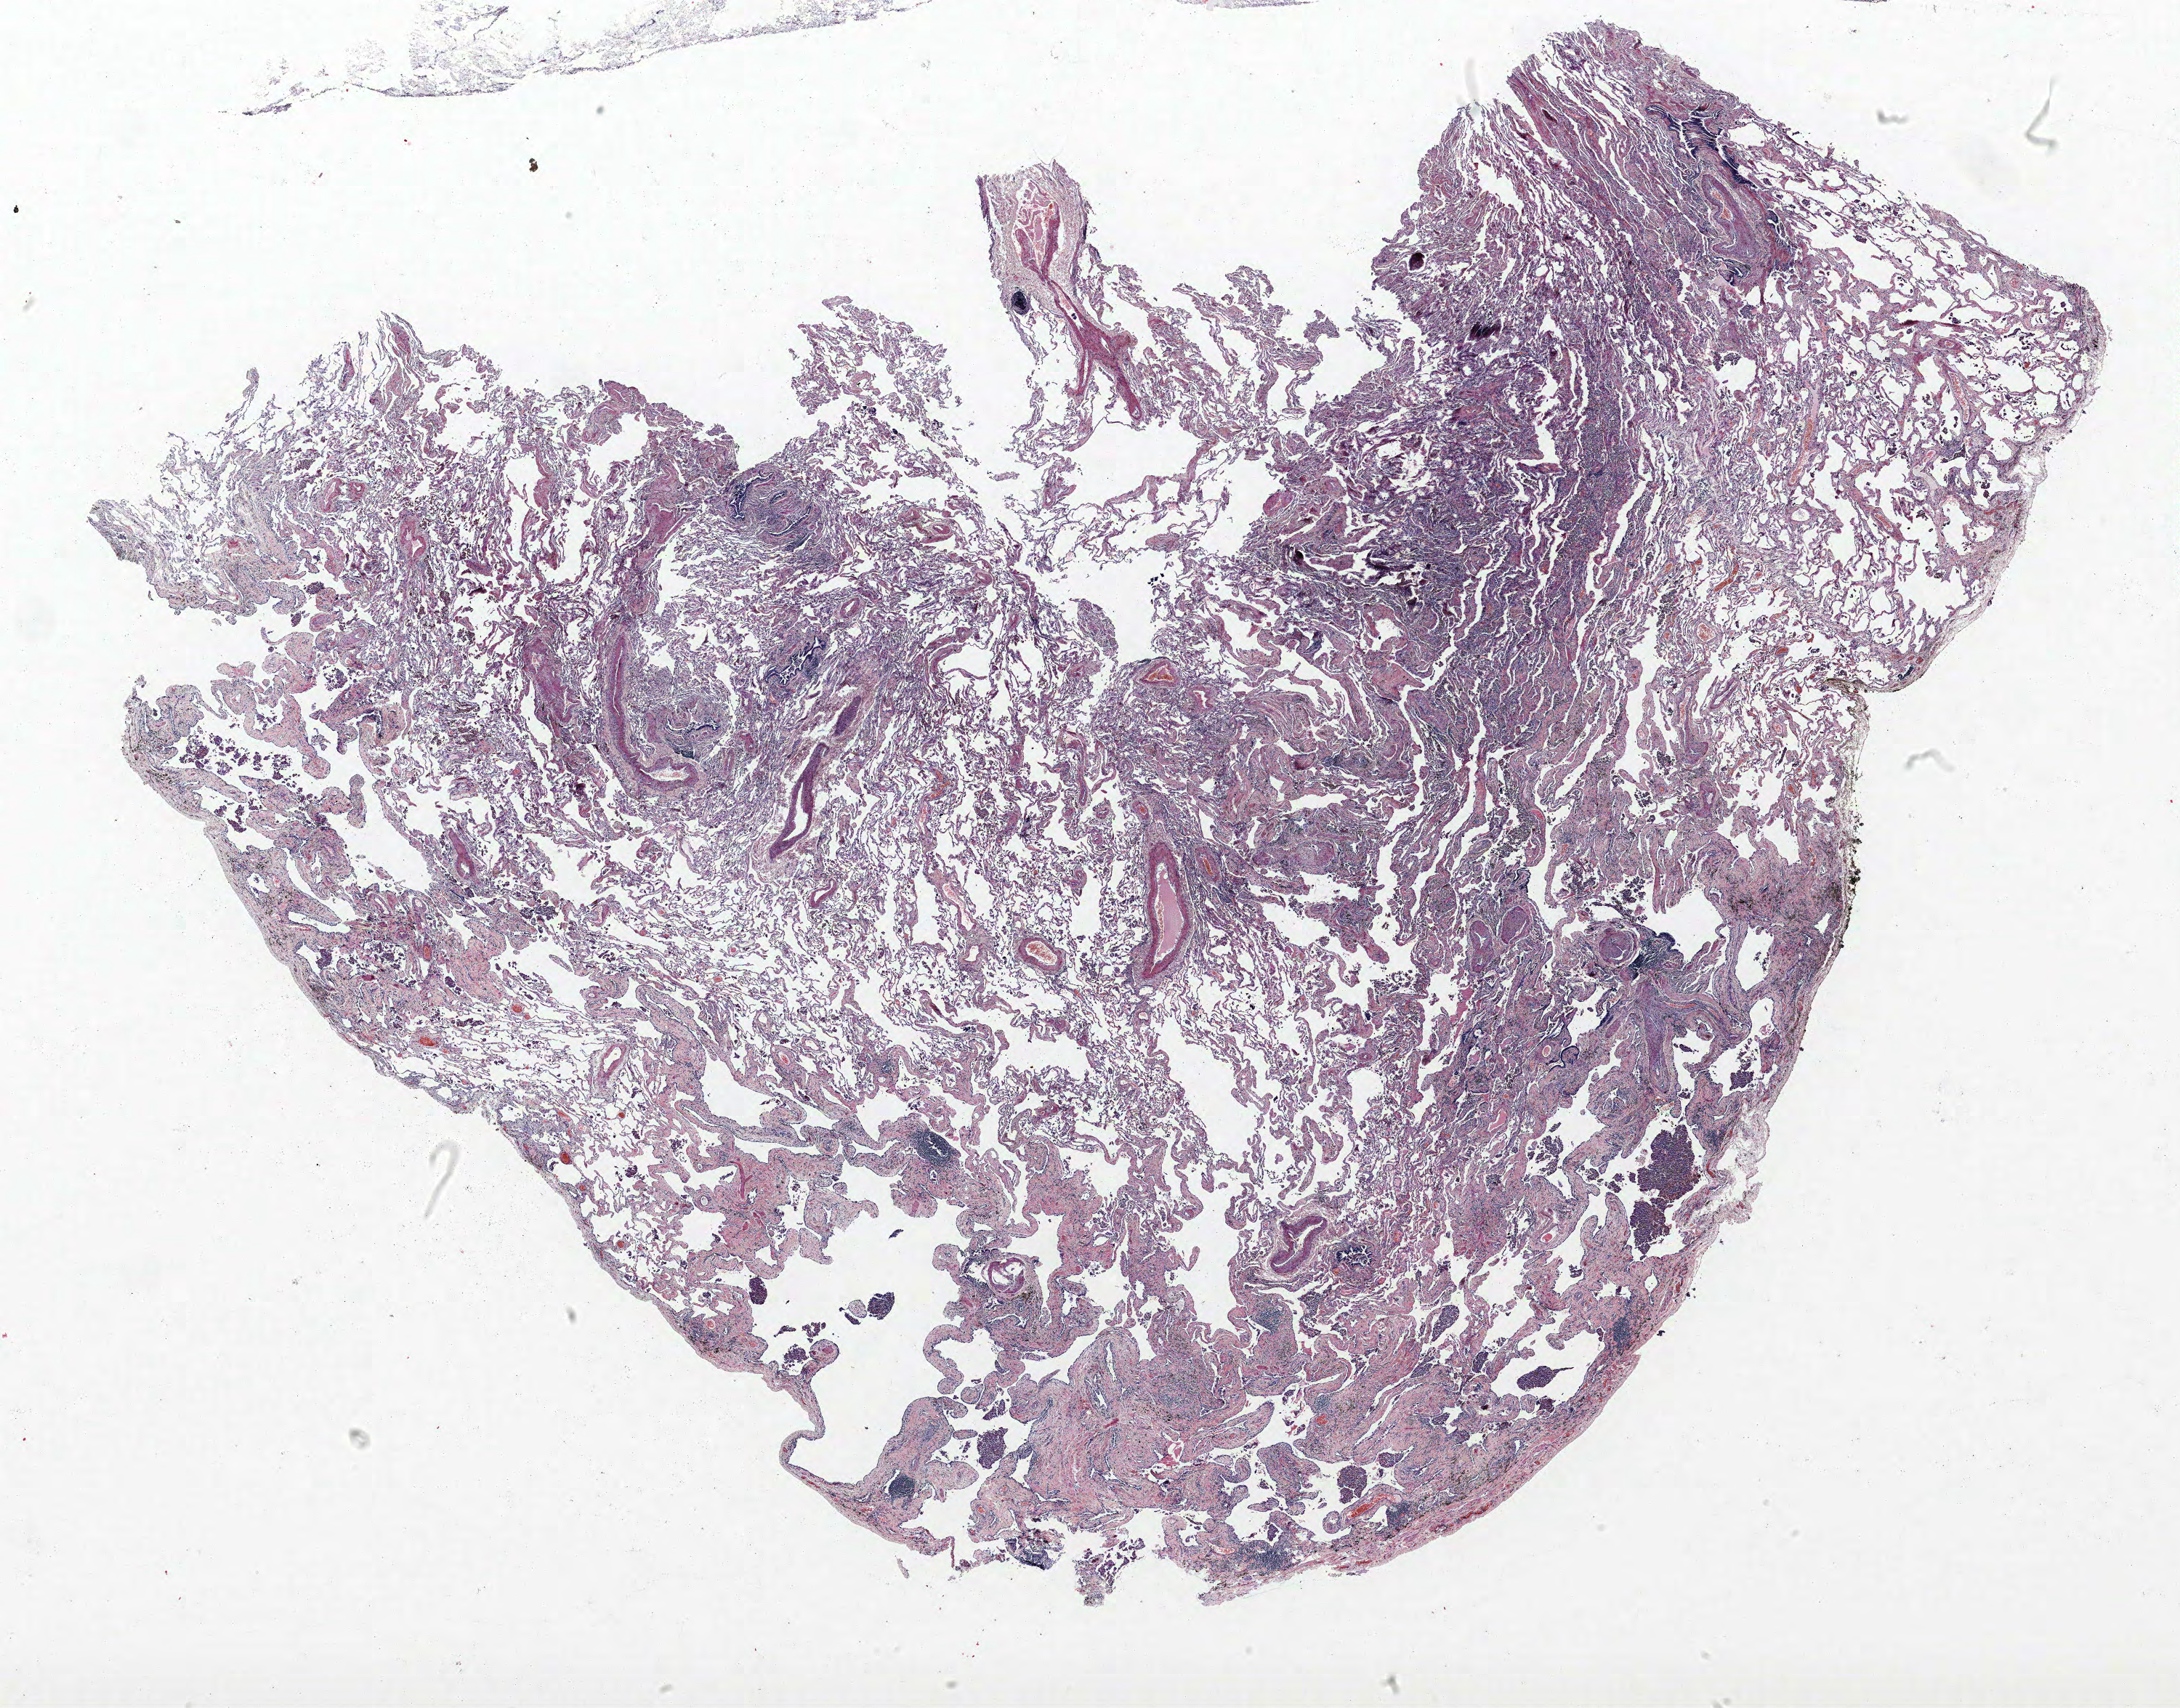
Hematoxylin and eosin (H&E) stained whole-slide image — whole scanned area (about 24.0 x 18.8 mm, acquisition: 40x scan) shown as a low-resolution overview, FFPE section, lung. Male patient, aged 64 at enrolment. Current smoker at enrolment. Grade: poorly differentiated (G3).
Tumour size (pathology): 11 mm. Stage (AJCC 6th edition): IIIA. Participant's lung-cancer diagnosis: Neuroendocrine carcinoma, NOS (ICD-O-3 8246/3). Primary tumour location (clinical record): left upper lobe.